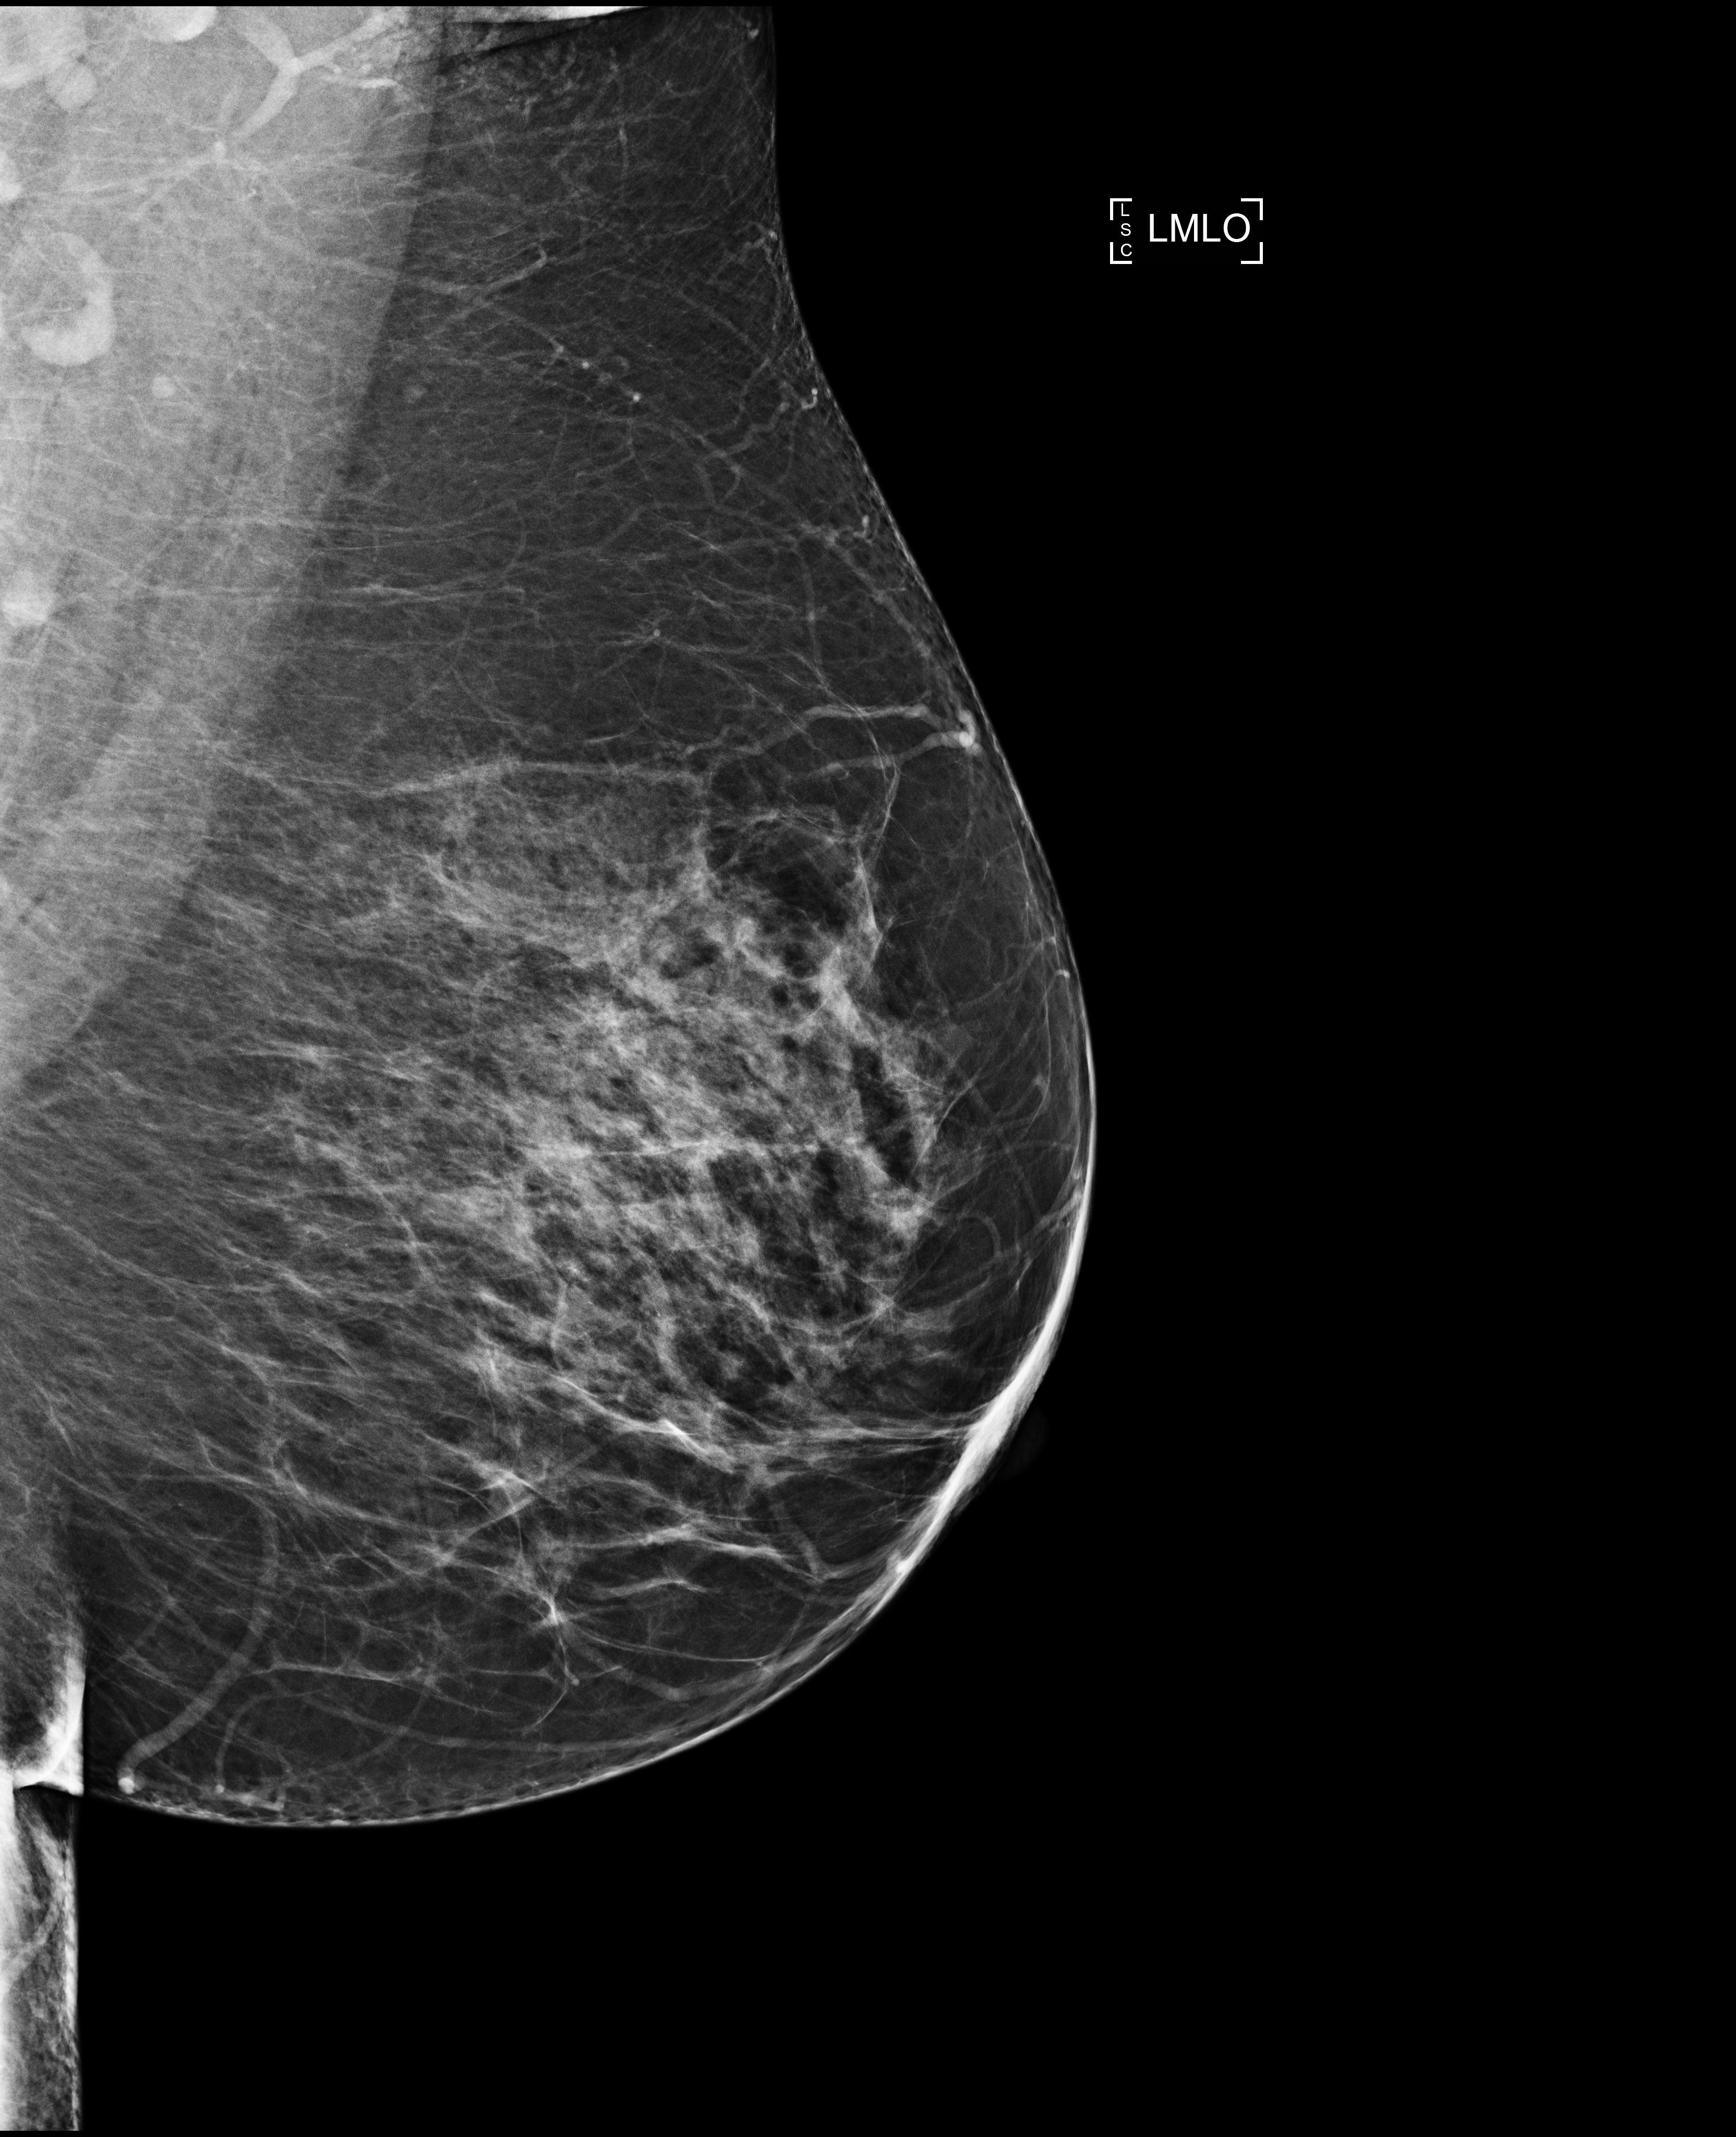
Full-field digital mammogram (FFDM), left breast, medio-lateral oblique projection, annual screening mammography examination, compressed breast thickness 70 mm, system: Selenia Dimensions. Patient: female, 57 years.
- BI-RADS breast density category at the screening exam (both breasts, scale 1–4): 3
- final BI-RADS assessment for this screening round (tomosynthesis exam, both breasts): category 2
- recall: no recall after this screen